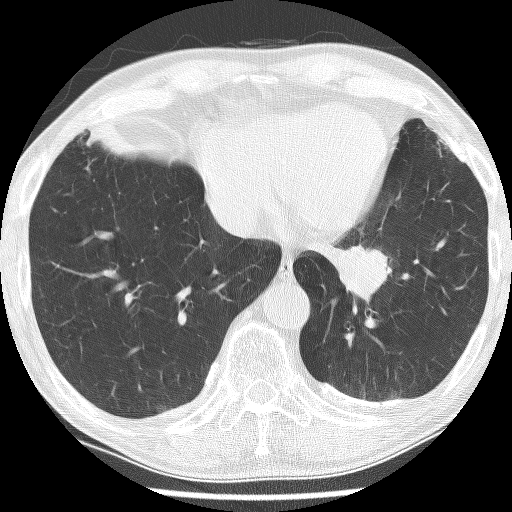
Axial slice from a low-dose chest CT screening exam. Baseline annual screen. Lung window (W 1500 / L -600 HU). 2.5 mm slice thickness. Male participant, aged 74 years at enrolment. Current smoker at enrolment.
Expert reader's lesion annotation, bounding box [x1, y1, x2, y2] px = [314, 221, 417, 314]. Reader record for this screening exam (exam-level; its link to the box is not recorded): non-calcified nodule or mass ≥4 mm, left lower lobe, 30 × 27 mm, spiculated (stellate) margins, soft tissue attenuation. Later outcome: lung cancer diagnosed 151 days after this screen — adenocarcinoma, NOS, left lower lobe, stage IIIA (AJCC 6th edition), 49 mm at pathology.